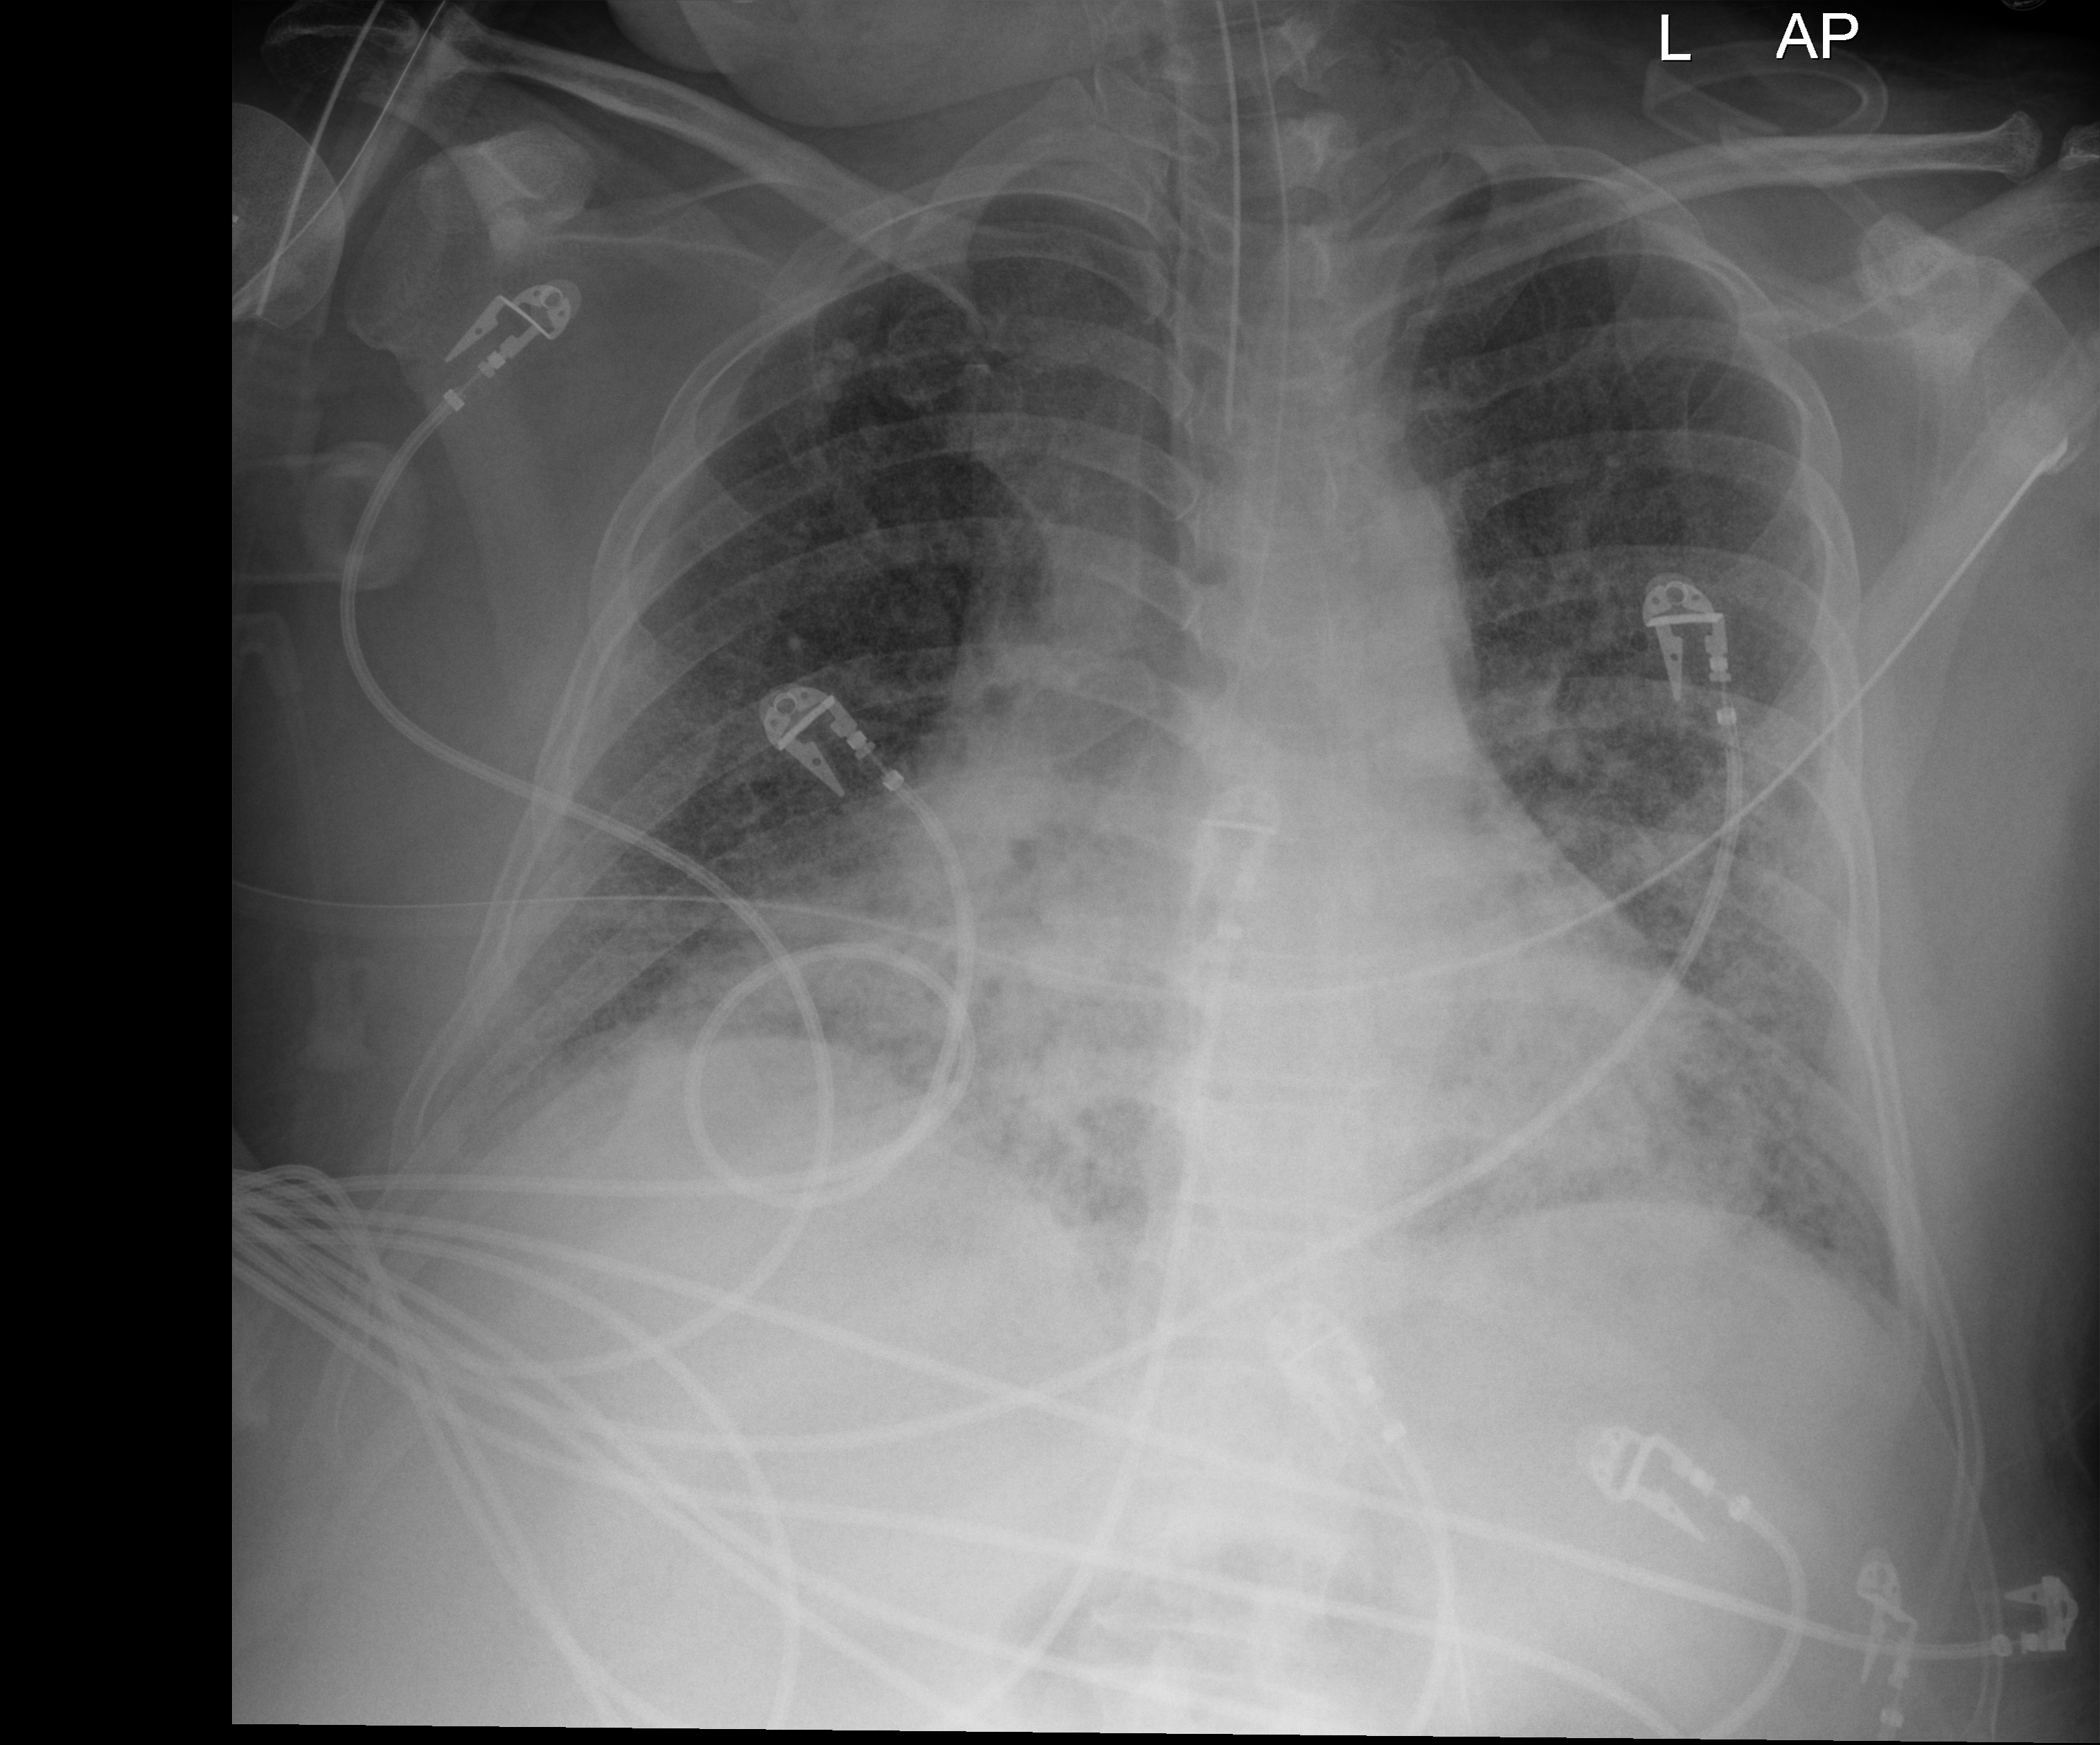
Portable chest radiograph, anteroposterior (AP) projection. Patient hospitalised with COVID-19, aged 18–59 years.
Admission-level facts for this patient (not findings on this image; timing relative to this image not recorded): hypertension (admission record): no.